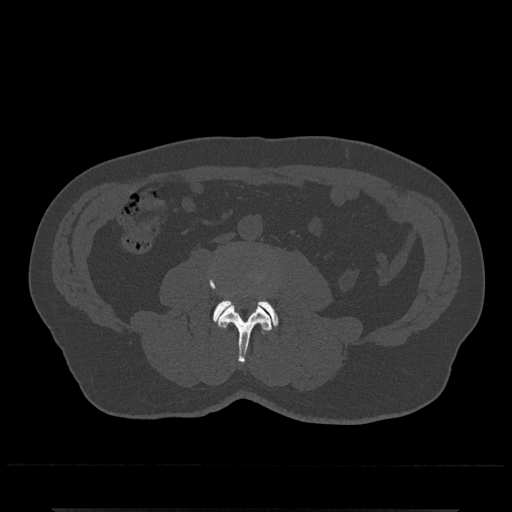
CT including the spine, one axial slice. Position 198 of 797 along the scan axis. Bone window (W 1800 / L 400 HU). 512 × 512 image matrix, field of view 393 × 393 mm. Patient: male, 67 years. Case-level facts recorded for this patient, not image findings: primary cancer: prostate.
Annotated regions visible in this slice (semi-automatic segmentation, software-assisted and operator-edited):
- L3 vertebra: bounding box (x1, y1, x2, y2) in pixels: (209, 273, 273, 363)
- L4 vertebra: (213, 299, 278, 326)